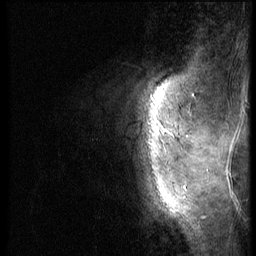
Breast MRI (dynamic contrast-enhanced), one sagittal slice; position 9 of 56 along the scan axis; dynamic contrast-enhanced series, image 2 of 3 at this slice position (ordered by acquisition); 1.5 T; TE 4.2 ms, TR 9 ms; 256 × 256 image matrix. Patient: female, 46 years. From the clinical record (not read from this slice): setting: breast cancer imaged before/during neoadjuvant chemotherapy; receptor status: HER2-positive.
Outlined on this slice (semi-automatically segmented with operator editing):
- analysis volume of interest (the breast-tissue region the enhancement analysis was run in; not a lesion): bounding box <114,98,174,182> (left, top, right, bottom; pixels)
- tumour enhancement mask (voxels above the 140 % enhancement threshold inside the analysis volume of interest): <166,129,170,132>